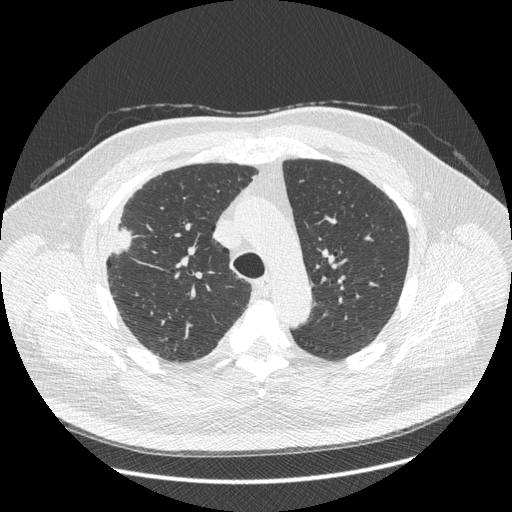
Axial slice from a low-dose chest CT screening exam. Third annual screen. Lung window (W 1500 / L -600 HU). 1.25 mm slice thickness. 512 × 512 image matrix. Male, age 66 years at enrolment.
- Lesion marked by an expert reader, bounding box [x1, y1, x2, y2] px = [88, 208, 148, 271].
- The exam's reader record, not a measurement of the box and not confirmed to be the same lesion: non-calcified nodule or mass ≥4 mm, right upper lobe, 48 × 25 mm, spiculated (stellate) margins, soft tissue attenuation, pre-existing on the prior screen: no.
- Official screen result: positive, other.
- Lung cancer was diagnosed 35 days after this screen: non-small cell carcinoma, right upper lobe, stage IV (AJCC 6th edition), 50 mm at pathology.